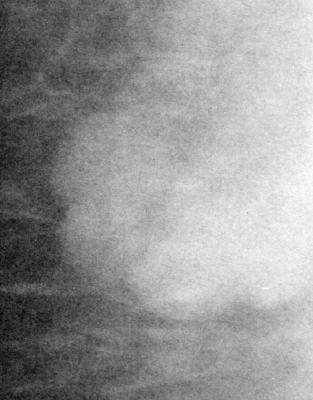
Cropped region of a digitized screen-film mammogram centred on a radiologist-marked abnormality; right breast; MLO view; BI-RADS breast density category 1 (scale 1–4).
Finding: mass, shape irregular, margins microlobulated; BI-RADS assessment category 5; subtlety rating 5 on a 1 (subtle) to 5 (obvious) scale; pathology result (as recorded, not read from the image): malignant.